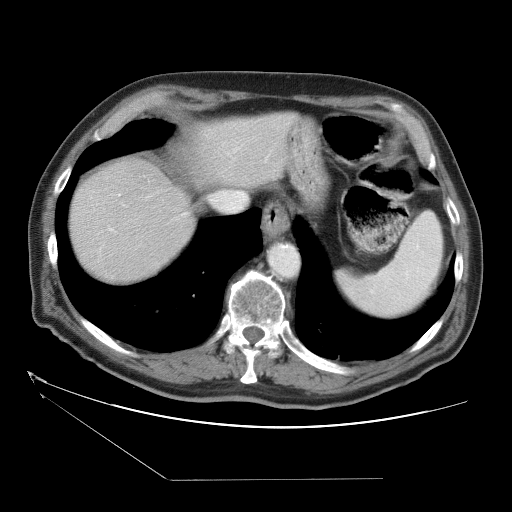
Contrast-enhanced abdominal CT (liver protocol), one axial slice; position 30 of 38 along the scan axis; reconstruction kernel STANDARD; one of 2 acquisitions stored at this slice position; soft-tissue window (W 400 / L 40 HU); 512 × 512 image matrix, field of view 400 × 400 mm. Case-level facts recorded for this patient, not image findings: diagnosis: hepatocellular carcinoma (patient treated with transarterial chemoembolisation; whether this scan precedes or follows treatment is not stated here); TNM stage (as recorded): Stage-II; Child-Pugh class: A; tumour differentiation: moderately differentiated; tumour nodularity: multinodular.
Annotated regions visible in this slice (semi-automatically segmented with operator editing):
- abdominal aorta: box from (x=270, y=246) to (x=298, y=276) px
- liver parenchyma outside the tumour (the mass and vessels are separate outlines, so this box may not span the whole liver): (x=70, y=112)–(x=312, y=282)
- liver vessels: (x=108, y=213)–(x=187, y=231)